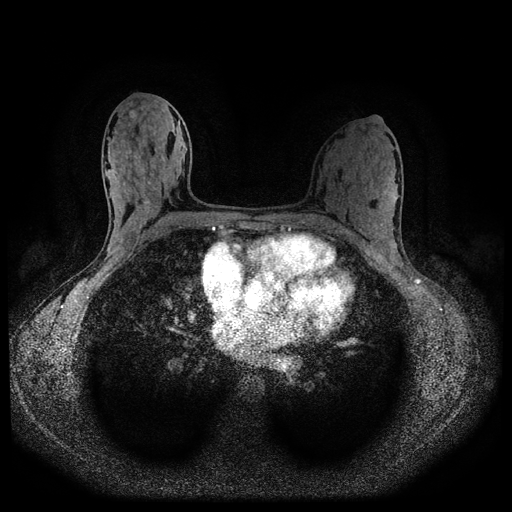
Breast MRI (dynamic contrast-enhanced, multi-phase), one axial slice. Slice 55 of 116 in the series (ordered by position). Dynamic contrast-enhanced series, time point 2 of 5 at this slice position (early post-contrast). 1.5 T. TE 2.7 ms, TR 5.4 ms. 512 × 512 image matrix, field of view 330 × 330 mm. Patient: female, 32 years.
Annotated regions visible in this slice (semi-automatically segmented with operator editing):
- breast lesion (labelled benign in the annotation): bounding box [x1, y1, x2, y2] px = [126, 108, 137, 119]